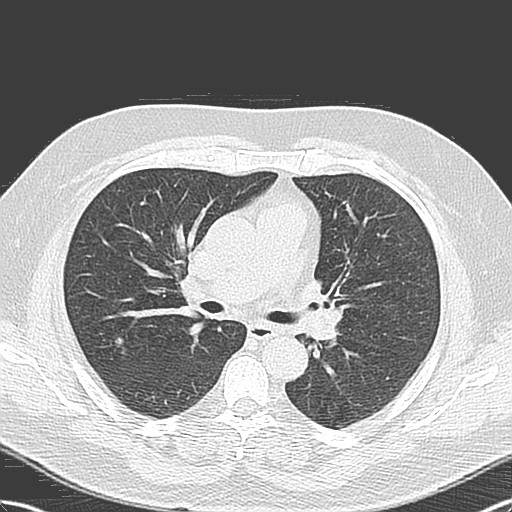
Low-dose screening chest CT, one axial slice. Slice 71 of 131 in the series (ordered by position). Lung window (W 1500 / L -600 HU). 3.2 mm slice thickness. 512 × 512 image matrix, field of view 356 × 356 mm.
Annotated regions visible in this slice (outlined manually by an expert reader):
- lesion 1 (tumor, upper lobe of right lung): box from (x=115, y=337) to (x=124, y=347) px